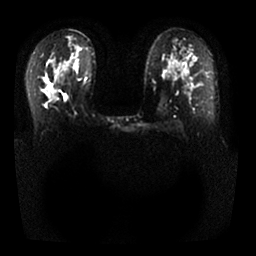
Breast MRI, one axial slice. Diffusion-weighted series; image 2 of 4 stored at this slice position (different b-values; order by instance number). 1.5 T. 4 mm slice thickness. 256 × 256 image matrix. Female patient.
Annotated regions visible in this slice (manually delineated by an expert):
- tumour on diffusion-weighted imaging: bounding box [x1, y1, x2, y2] px = [44, 88, 55, 103]